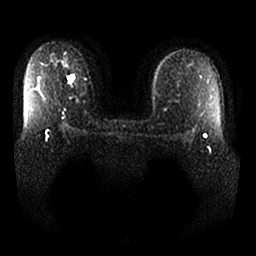
Breast MRI, one axial slice. Diffusion-weighted series; image 2 of 4 stored at this slice position (different b-values; order by instance number). 1.5 T. 4 mm slice thickness. 256 × 256 image matrix. Female patient.
Outlined on this slice (outlined manually by an expert reader):
- tumour on diffusion-weighted imaging: bounding box [x1, y1, x2, y2] px = [66, 73, 75, 84]